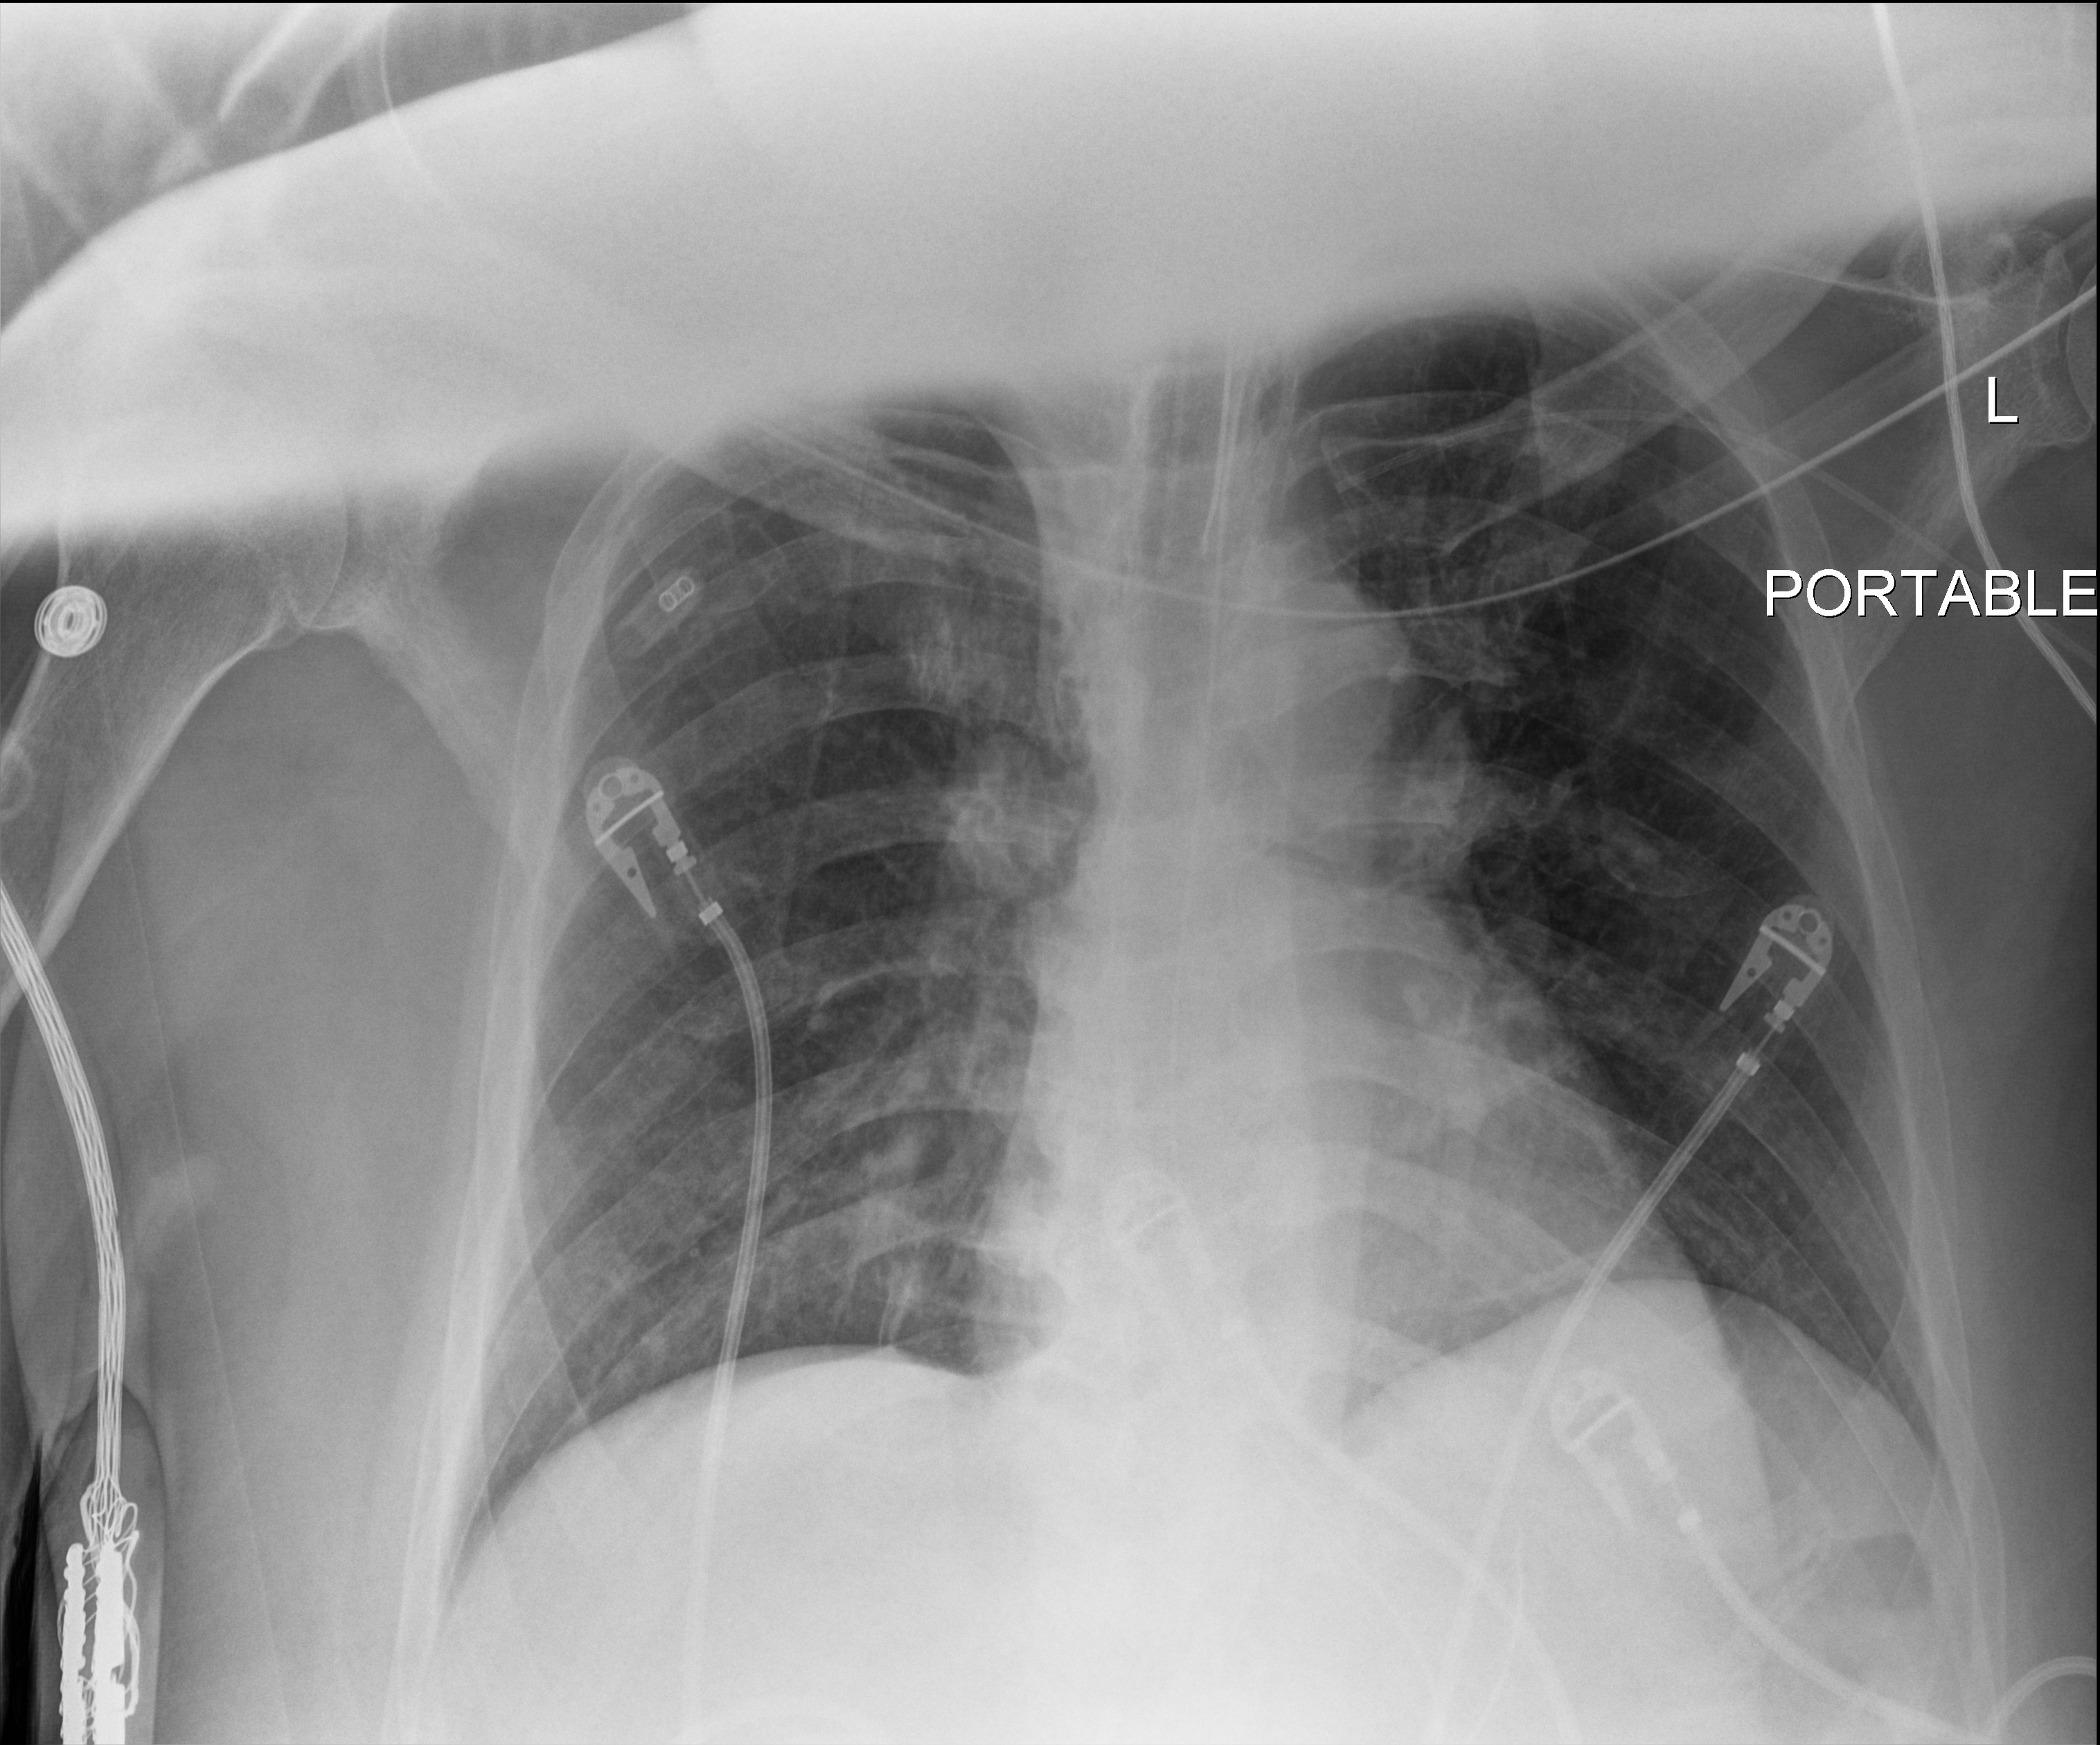
Bedside chest radiograph (digital radiography). Adult patient hospitalised with COVID-19, age 18–59 years.
Hospital-stay facts (about this admission, not read from this image; timing relative to this image not recorded):
- length of hospital stay: 37 days
- hypertension (admission record): no
- diabetes (admission record): yes